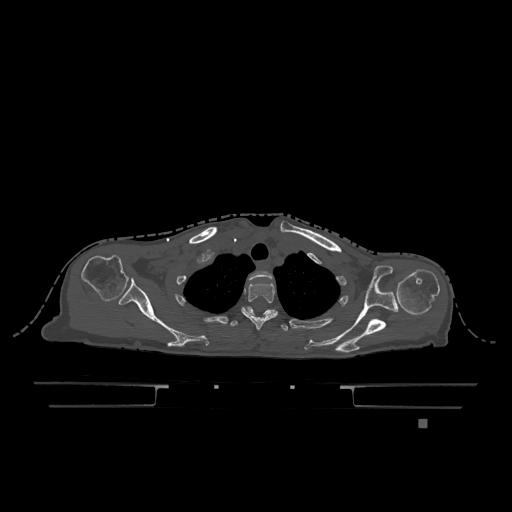
CT including the spine, one axial slice; slice 956 of 1317 in the series (ordered by position); bone window (W 1800 / L 400 HU); 512 × 512 image matrix, field of view 500 × 500 mm. Female patient, age 74 years. From the clinical record (not read from this slice): primary cancer: lung; vertebrae with lytic lesions (as recorded): T1, T4, T5, T6, L4, L5.
Annotated regions visible in this slice (semi-automatically segmented with operator editing):
- T1 vertebra: bounding box [x1, y1, x2, y2] px = [249, 271, 273, 280]
- T2 vertebra: [241, 282, 278, 330]
- T3 vertebra: [230, 308, 288, 331]
- T6 vertebra: [242, 306, 276, 316]